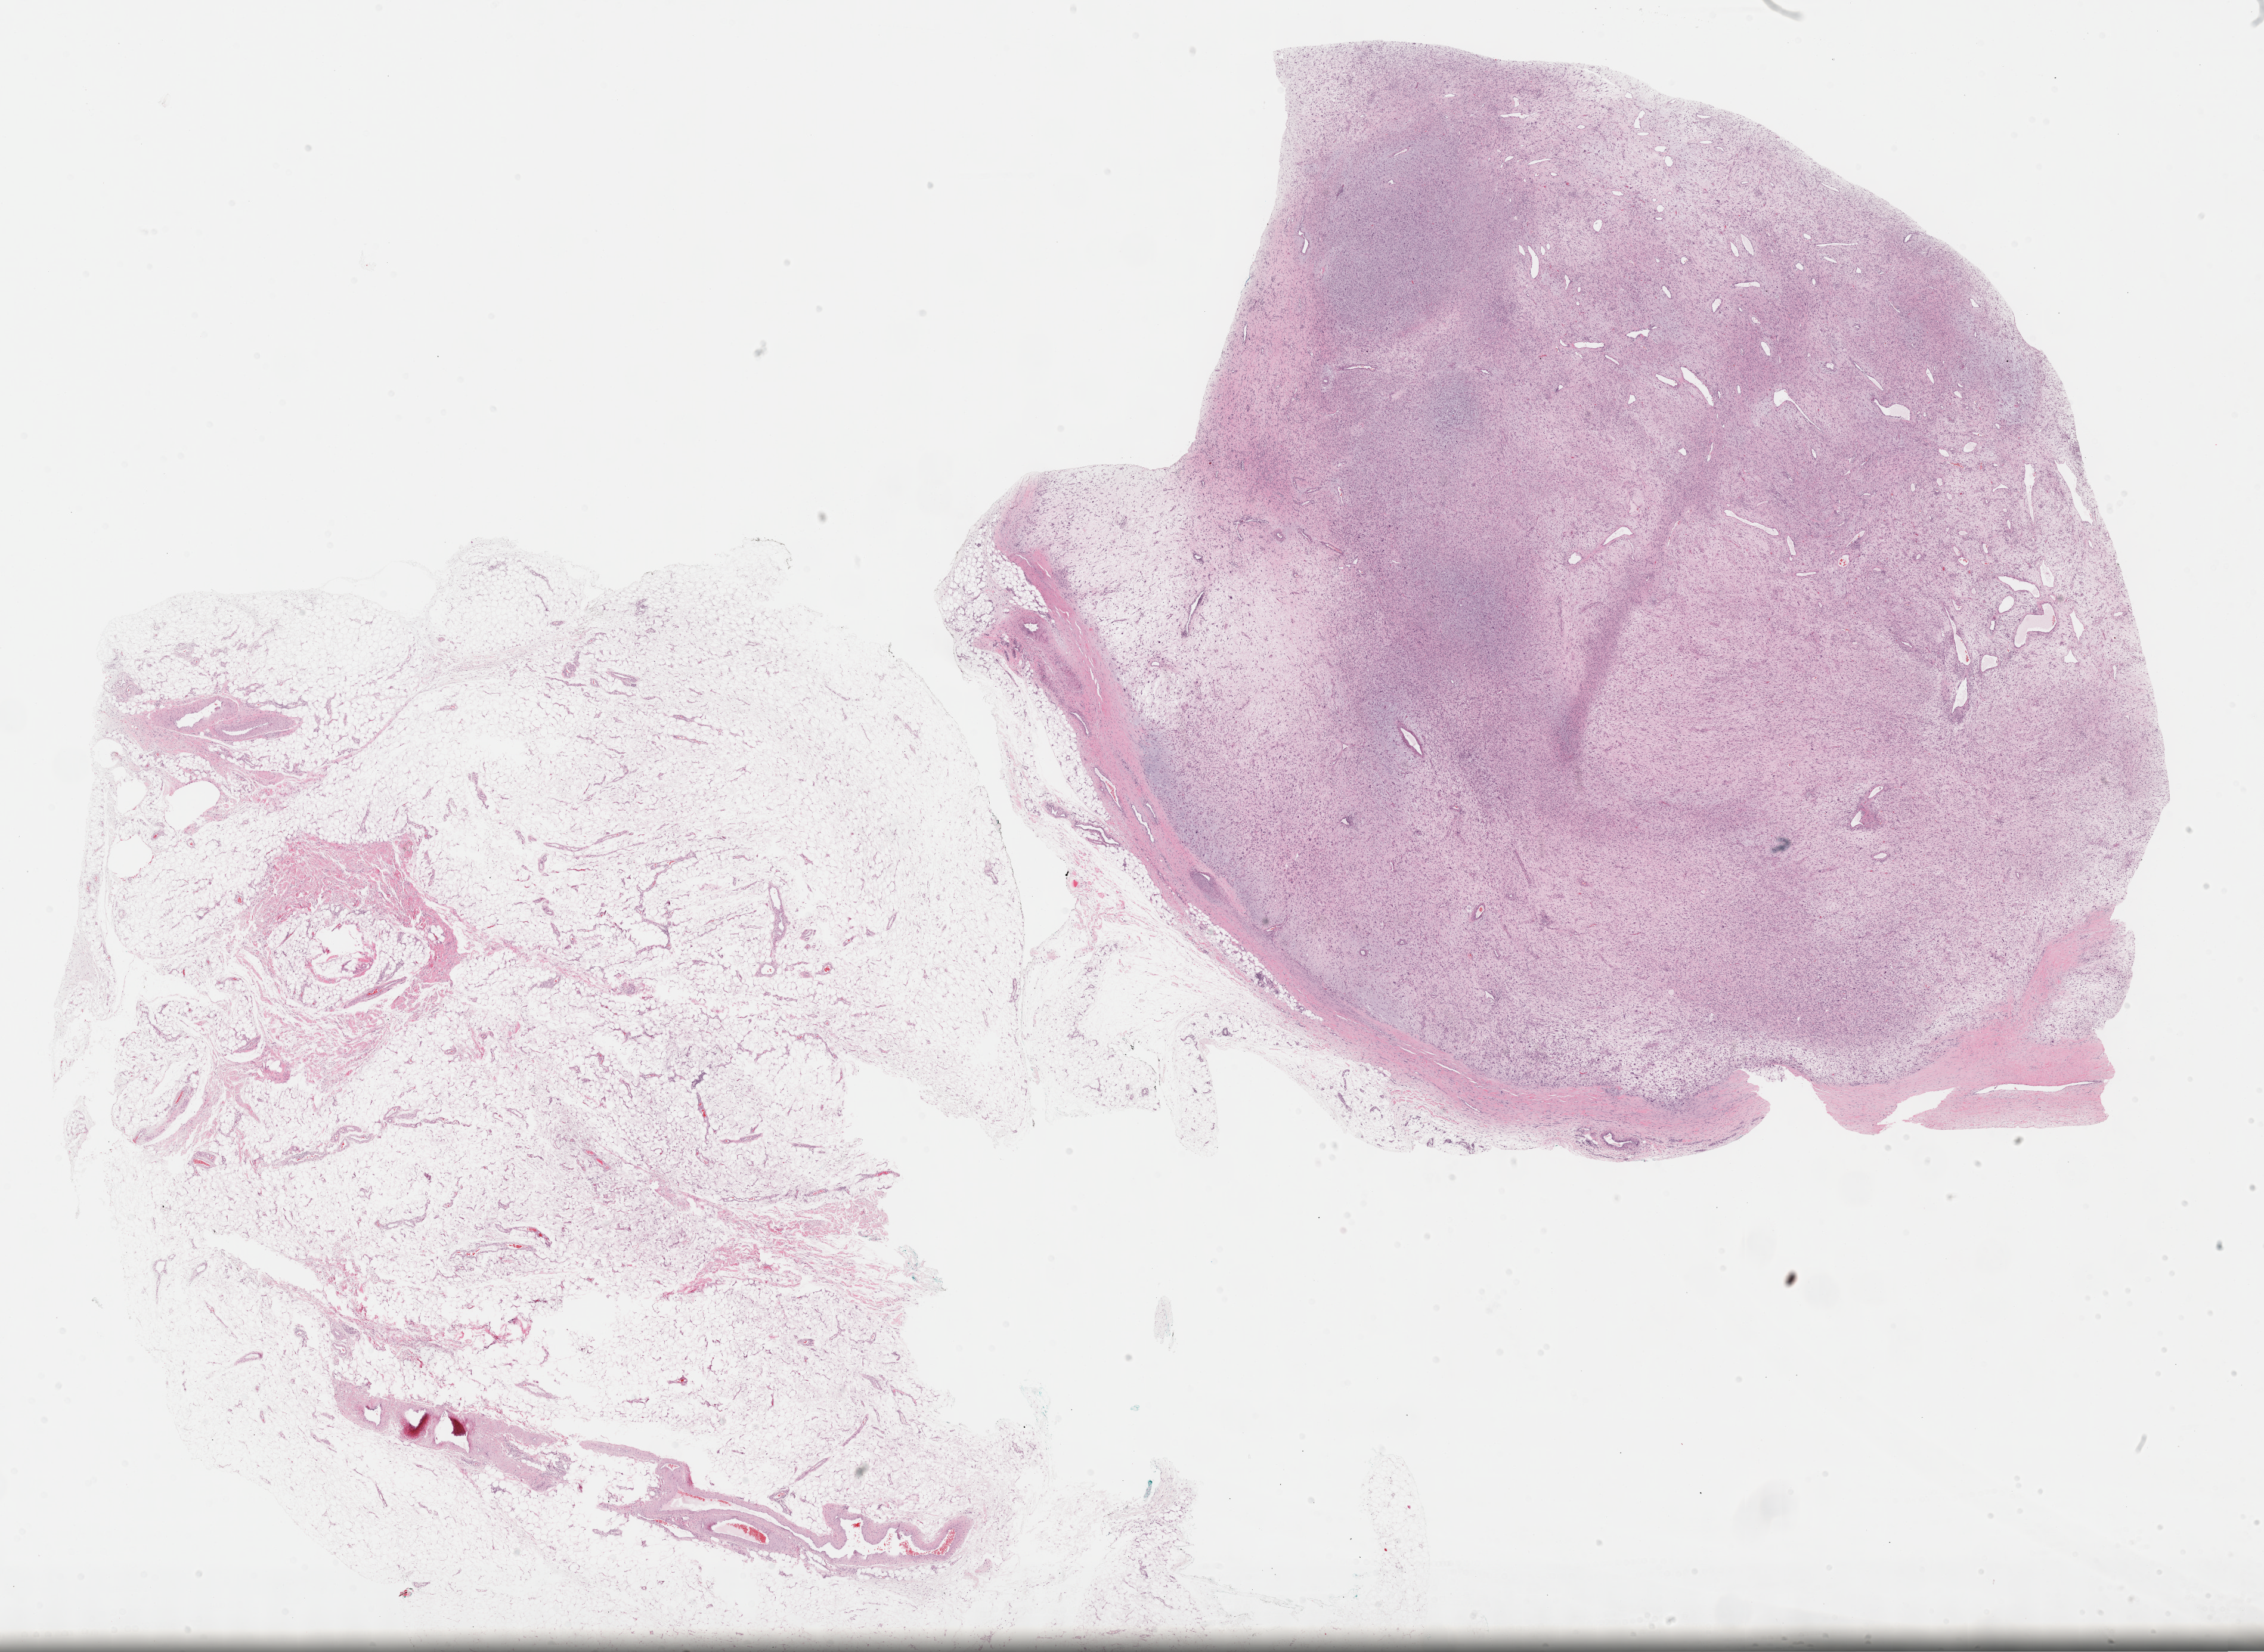
Digitized H&E tissue section (whole slide), a low-resolution overview of the entire scanned area, about 30.7 x 22.4 mm (slide scanned at 40x). FFPE section. Sample: primary tumour, connective, subcutaneous and other soft tissues. Female patient; age at initial diagnosis 31 years.
Pathologic diagnosis: Fibromyxosarcoma.